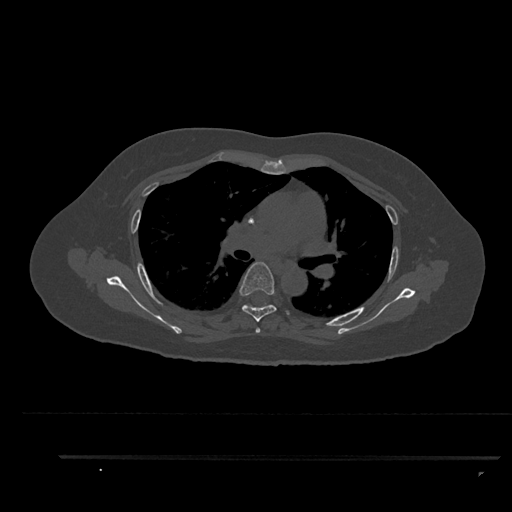
CT including the spine, one axial slice; position 598 of 797 along the scan axis; reconstruction kernel Br40s/3; 120 kVp; bone window (W 1800 / L 400 HU); 0.5 mm slice thickness; 512 × 512 image matrix, field of view 408 × 408 mm. Female patient, age 44 years. From the clinical record (not read from this slice): primary cancer: renal.
Outlined on this slice (semi-automatically segmented with operator editing):
- T4 vertebra: bounding box [x1, y1, x2, y2] px = [255, 328, 260, 333]
- T5 vertebra: [239, 262, 289, 322]
- T6 vertebra: [242, 303, 269, 307]